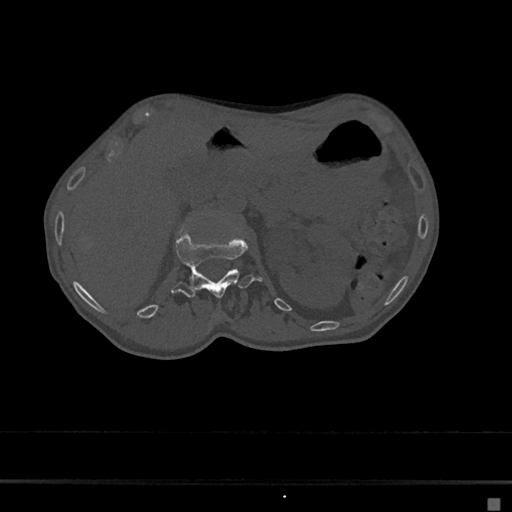
CT including the spine, one axial slice. 120 kVp. Bone window (W 1800 / L 400 HU). 0.5 mm slice thickness. 512 × 512 image matrix, field of view 360 × 360 mm. Female patient, age 68 years. Case-level facts recorded for this patient, not image findings: primary cancer: renal.
Outlined on this slice (semi-automatically segmented with operator editing):
- L1 vertebra: bounding box [x1, y1, x2, y2] px = [172, 229, 263, 299]